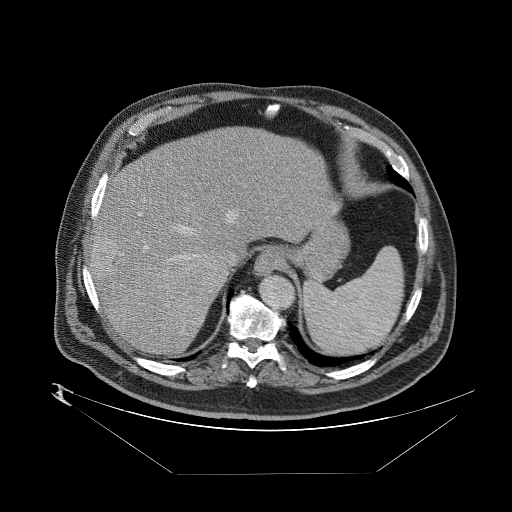
Contrast-enhanced abdominal CT (liver protocol), one axial slice. Position 64 of 89 along the scan axis. Reconstruction kernel STANDARD. 140 kVp. One of 2 acquisitions stored at this slice position. Soft-tissue window (W 400 / L 40 HU). 2.5 mm slice thickness. 512 × 512 image matrix, field of view 480 × 480 mm. From the clinical record (not read from this slice): diagnosis: hepatocellular carcinoma (patient treated with transarterial chemoembolisation; whether this scan precedes or follows treatment is not stated here); TNM stage (as recorded): Stage-II; Child-Pugh class: B; tumour differentiation: moderately differentiated; tumour nodularity: multinodular.
Annotated regions visible in this slice (semi-automatically segmented with operator editing):
- abdominal aorta: bounding box (x1, y1, x2, y2) in pixels: (260, 277, 294, 310)
- liver parenchyma outside the tumour (the mass and vessels are separate outlines, so this box may not span the whole liver): (90, 124, 338, 352)
- mass: (92, 241, 227, 321)
- liver vessels: (93, 205, 215, 323)